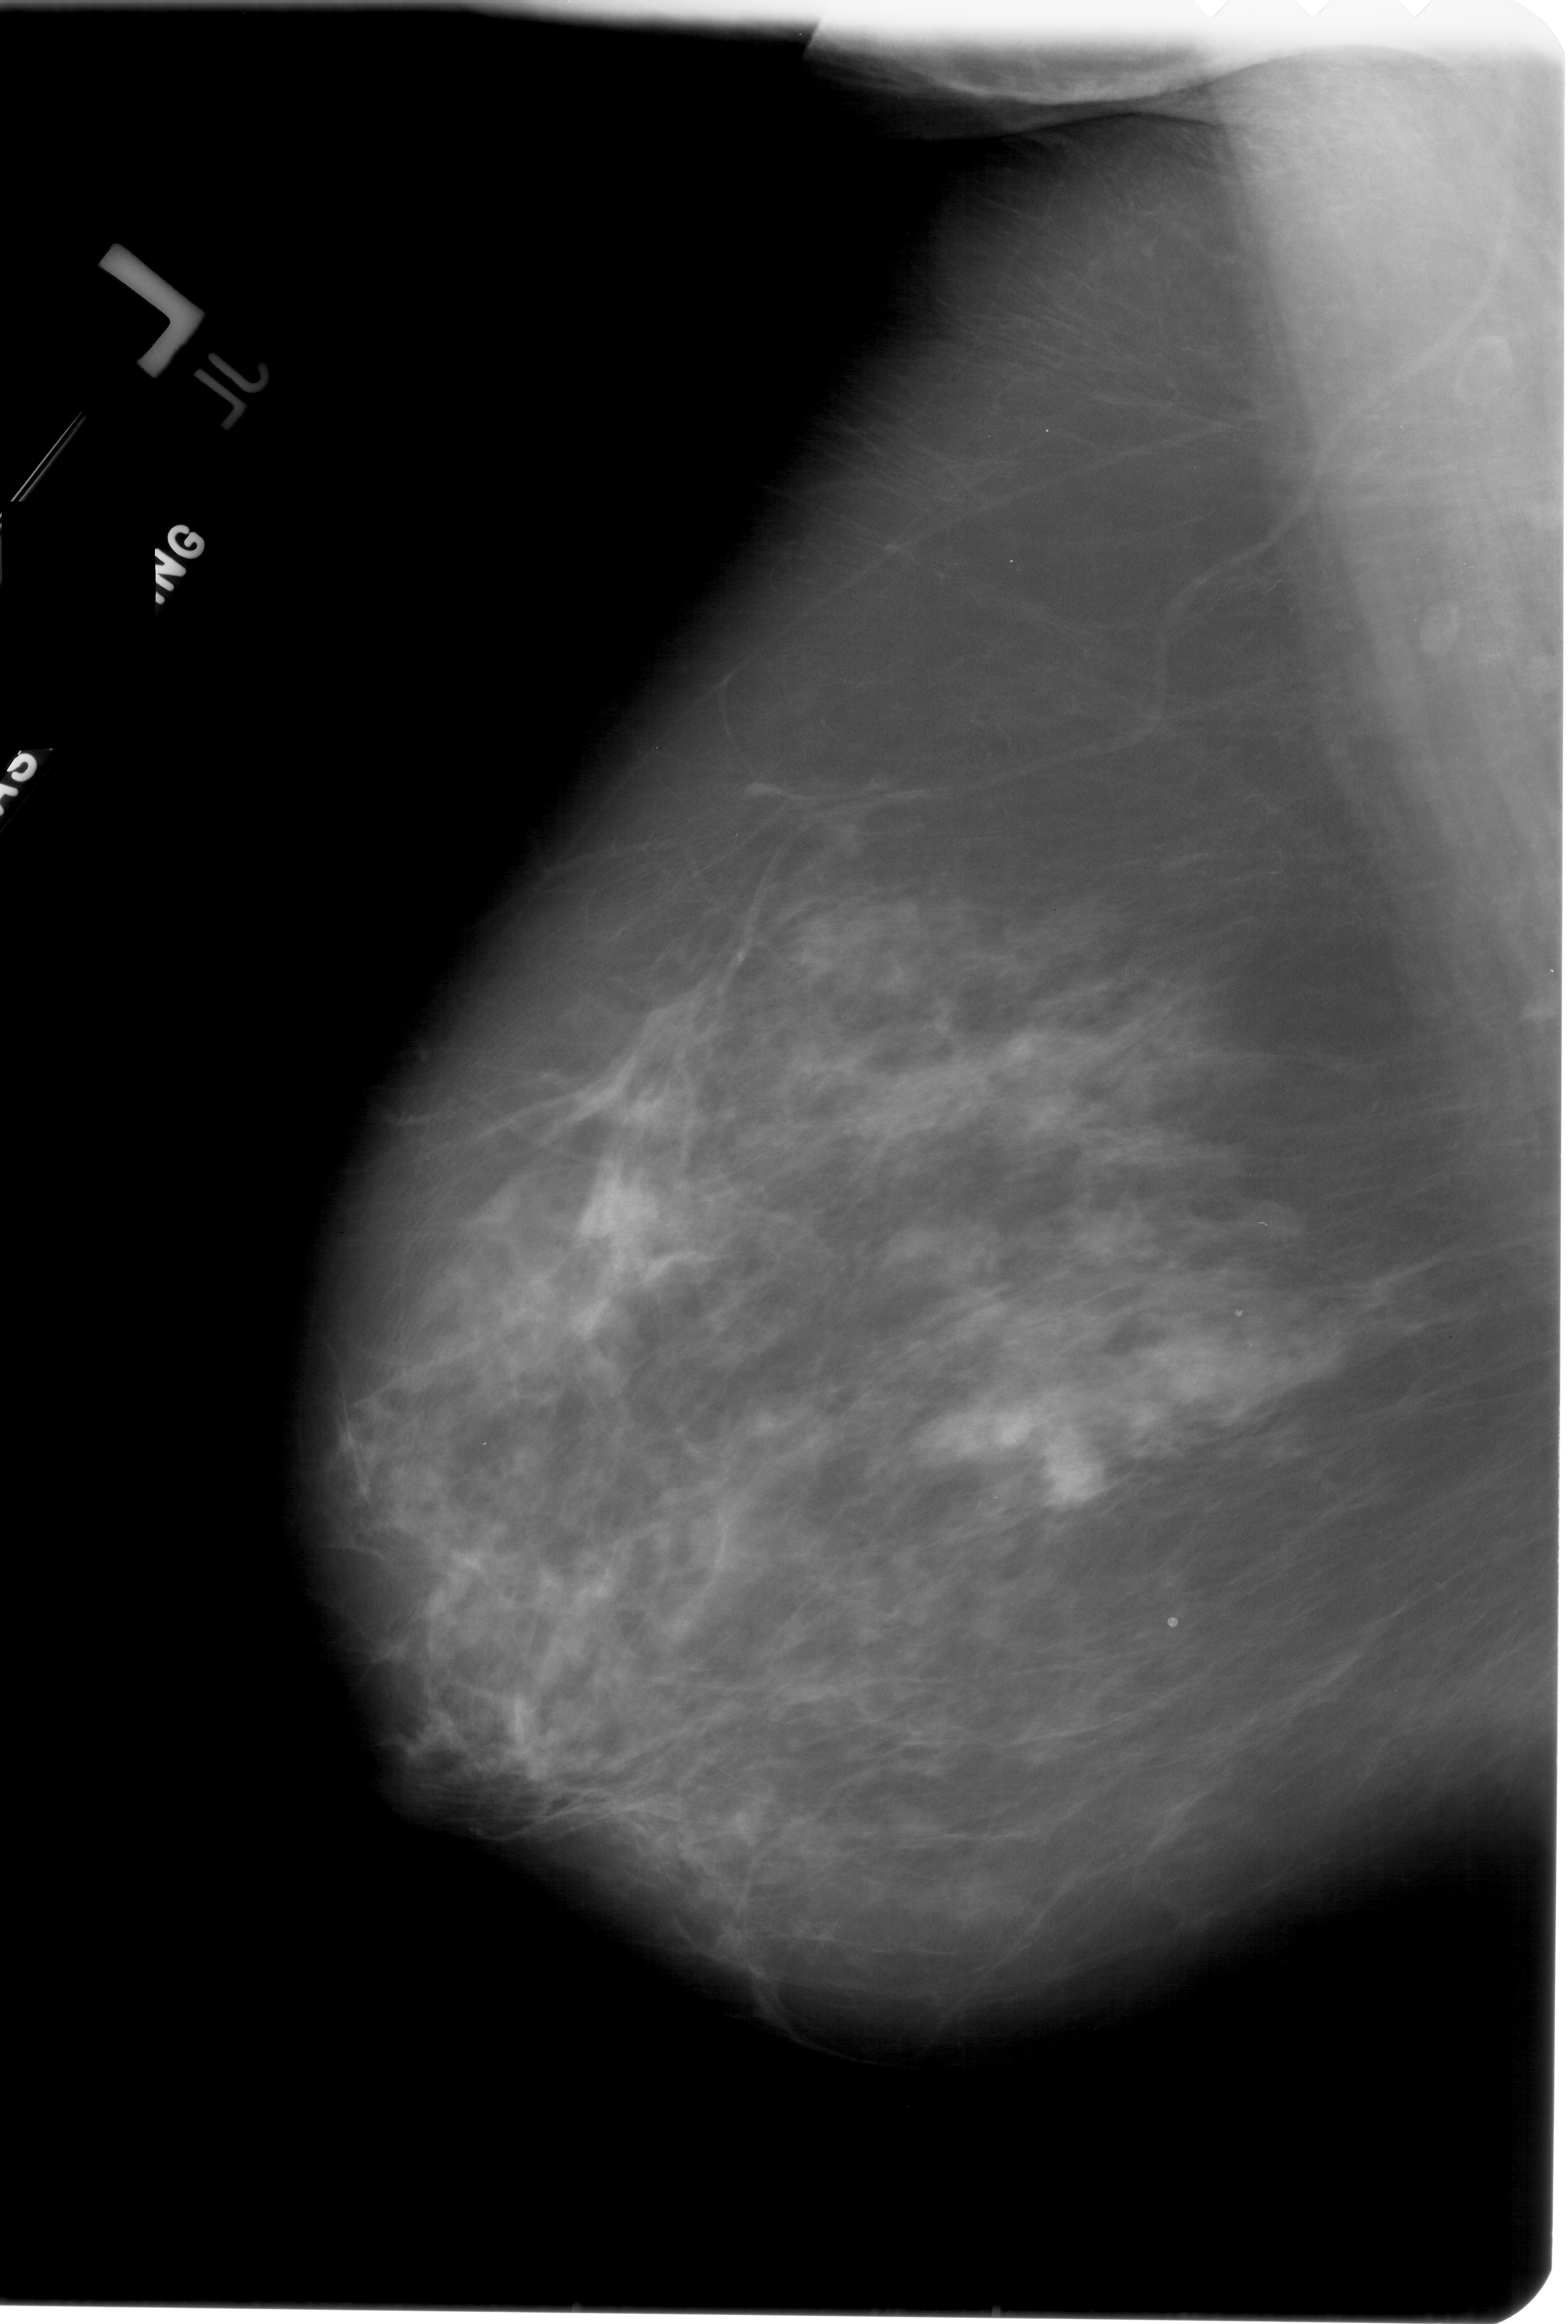
Mammogram (digitized film); left breast; MLO view; 1568 × 2324 image matrix.
Expert-marked regions of interest on this image (one box per marked abnormality):
- mass, shape irregular, margins spiculated; BI-RADS assessment category 5; subtlety rating 5 on a 1 (subtle) to 5 (obvious) scale; pathology result (as recorded, not read from the image): malignant: bounding box (x1, y1, x2, y2) in pixels: (1034, 1440, 1110, 1514)